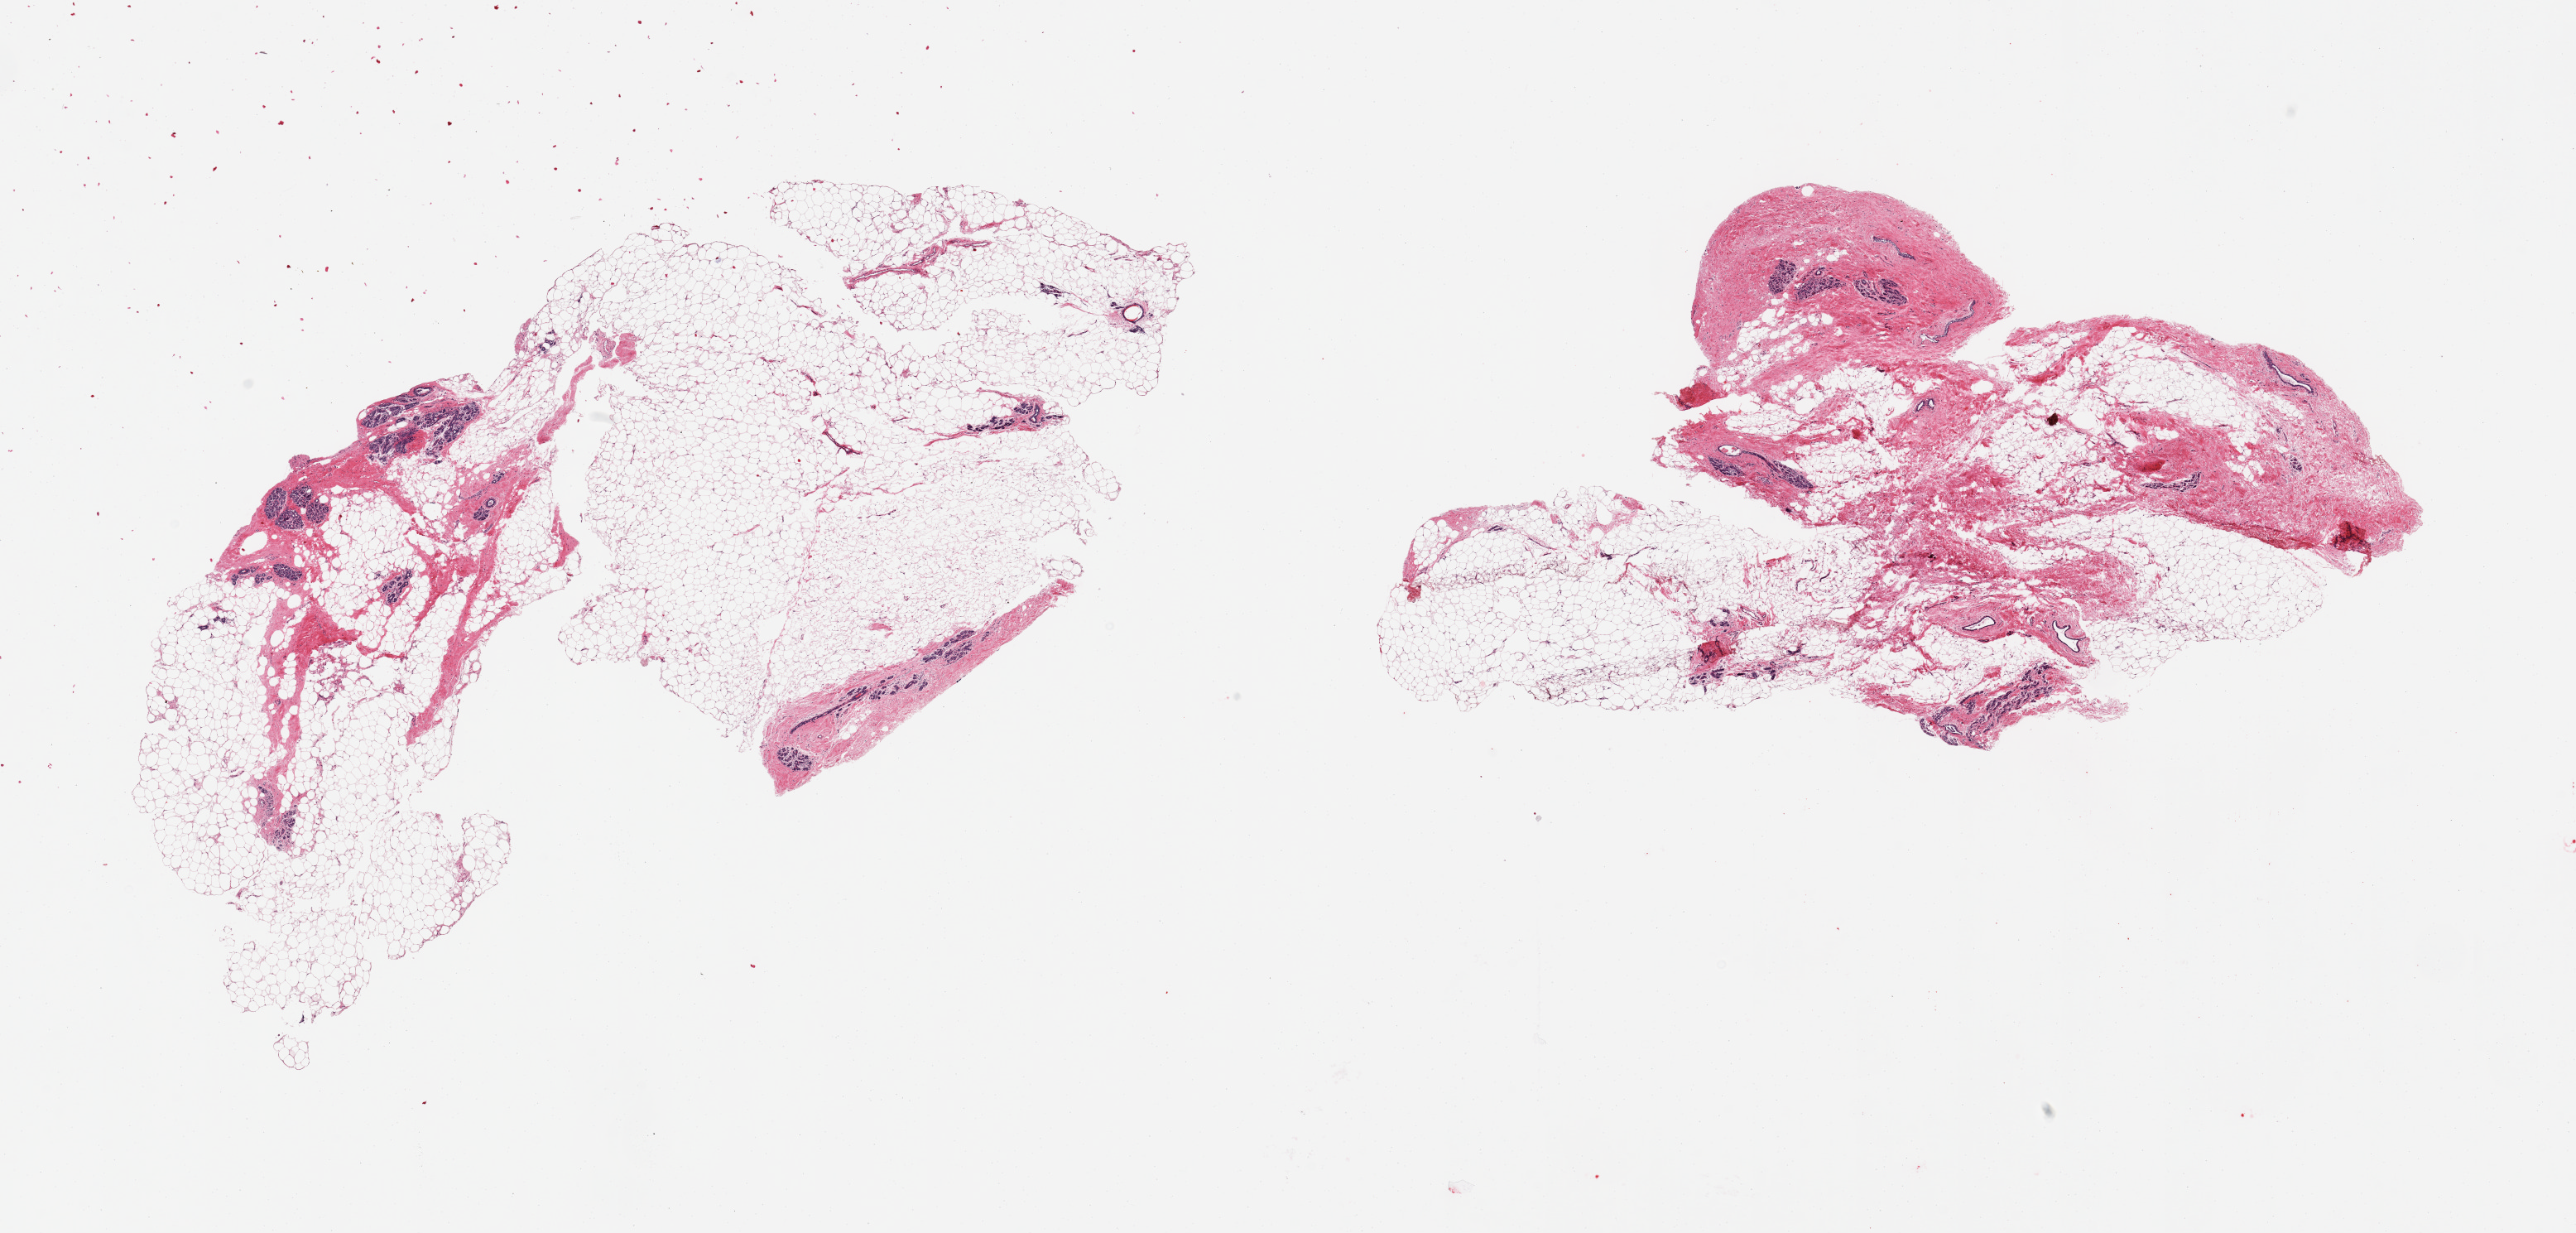
Hematoxylin and eosin (H&E) whole-slide image, low-resolution overview of the scanned area, about 24.6 x 11.8 mm. PAXgene-fixed paraffin-embedded (PFPE) section. Section of breast (target tissue). Donor tissue sample. Donor: female.
Pathologist's review note for this sample: 2 pieces; lobules and ducts embedded in fibroadipose tissue.